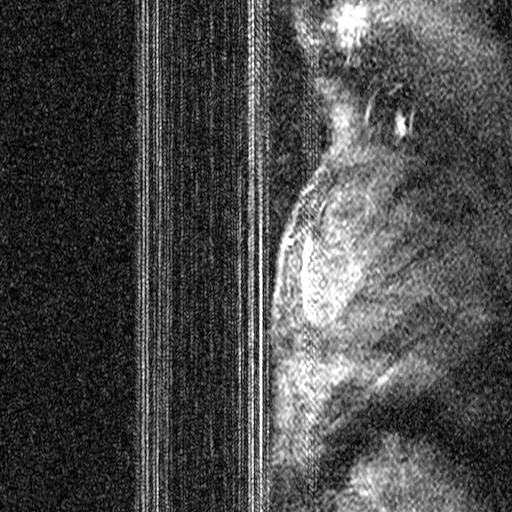
Breast MRI (dynamic contrast-enhanced), one sagittal slice; slice 35 of 44 in the series (ordered by position); dynamic contrast-enhanced study with each time point stored as its own series, time point 2 of 3 at this slice position (early post-contrast, ordered by acquisition time); 1.5 T; TE 4.5 ms, TR 11 ms; 3 mm slice thickness; 512 × 512 image matrix, field of view 200 × 200 mm. Patient: female, 44 years. Case-level facts recorded for this patient, not image findings: setting: breast cancer imaged before/during neoadjuvant chemotherapy; receptor status: HR-positive, HER2-negative.
Outlined on this slice (semi-automatically segmented with operator editing):
- analysis volume of interest (the breast-tissue region the enhancement analysis was run in; not a lesion): bounding box [x1, y1, x2, y2] px = [206, 164, 319, 299]
- tumour enhancement mask (voxels above the 90 % enhancement threshold inside the analysis volume of interest): [259, 164, 314, 272]